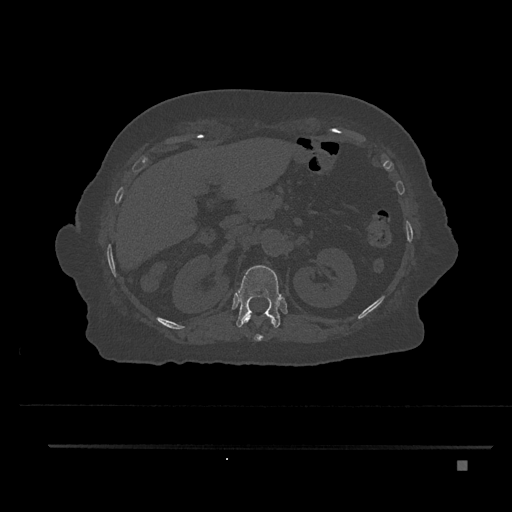
CT including the spine, one axial slice. Slice 276 of 797 in the series (ordered by position). 120 kVp. Bone window (W 1800 / L 400 HU). 0.5 mm slice thickness. 512 × 512 image matrix, field of view 437 × 437 mm. Patient: female, 76 years. Case-level facts recorded for this patient, not image findings: primary cancer: lung.
Annotated regions visible in this slice (semi-automatically segmented with operator editing):
- T11 vertebra: bounding box [x1, y1, x2, y2] px = [242, 313, 274, 341]
- T12 vertebra: [236, 265, 282, 329]